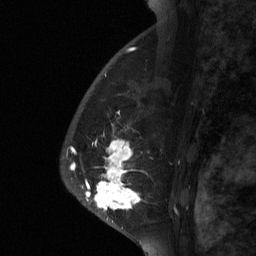
Breast MRI (dynamic contrast-enhanced), one sagittal slice; position 45 of 64 along the scan axis; dynamic contrast-enhanced study with each time point stored as its own series, time point 2 of 3 at this slice position (early post-contrast, ordered by acquisition time); 1.5 T; TE 4.8 ms, TR 27 ms; 2 mm slice thickness; 256 × 256 image matrix. Patient: female, 56 years. From the clinical record (not read from this slice): setting: breast cancer imaged before/during neoadjuvant chemotherapy; receptor status: HER2-positive.
Annotated regions visible in this slice (semi-automatic segmentation, software-assisted and operator-edited):
- analysis volume of interest (the breast-tissue region the enhancement analysis was run in; not a lesion): box from (x=81, y=104) to (x=182, y=229) px
- tumour enhancement mask (voxels above the 90 % enhancement threshold inside the analysis volume of interest): (x=85, y=139)–(x=141, y=210)